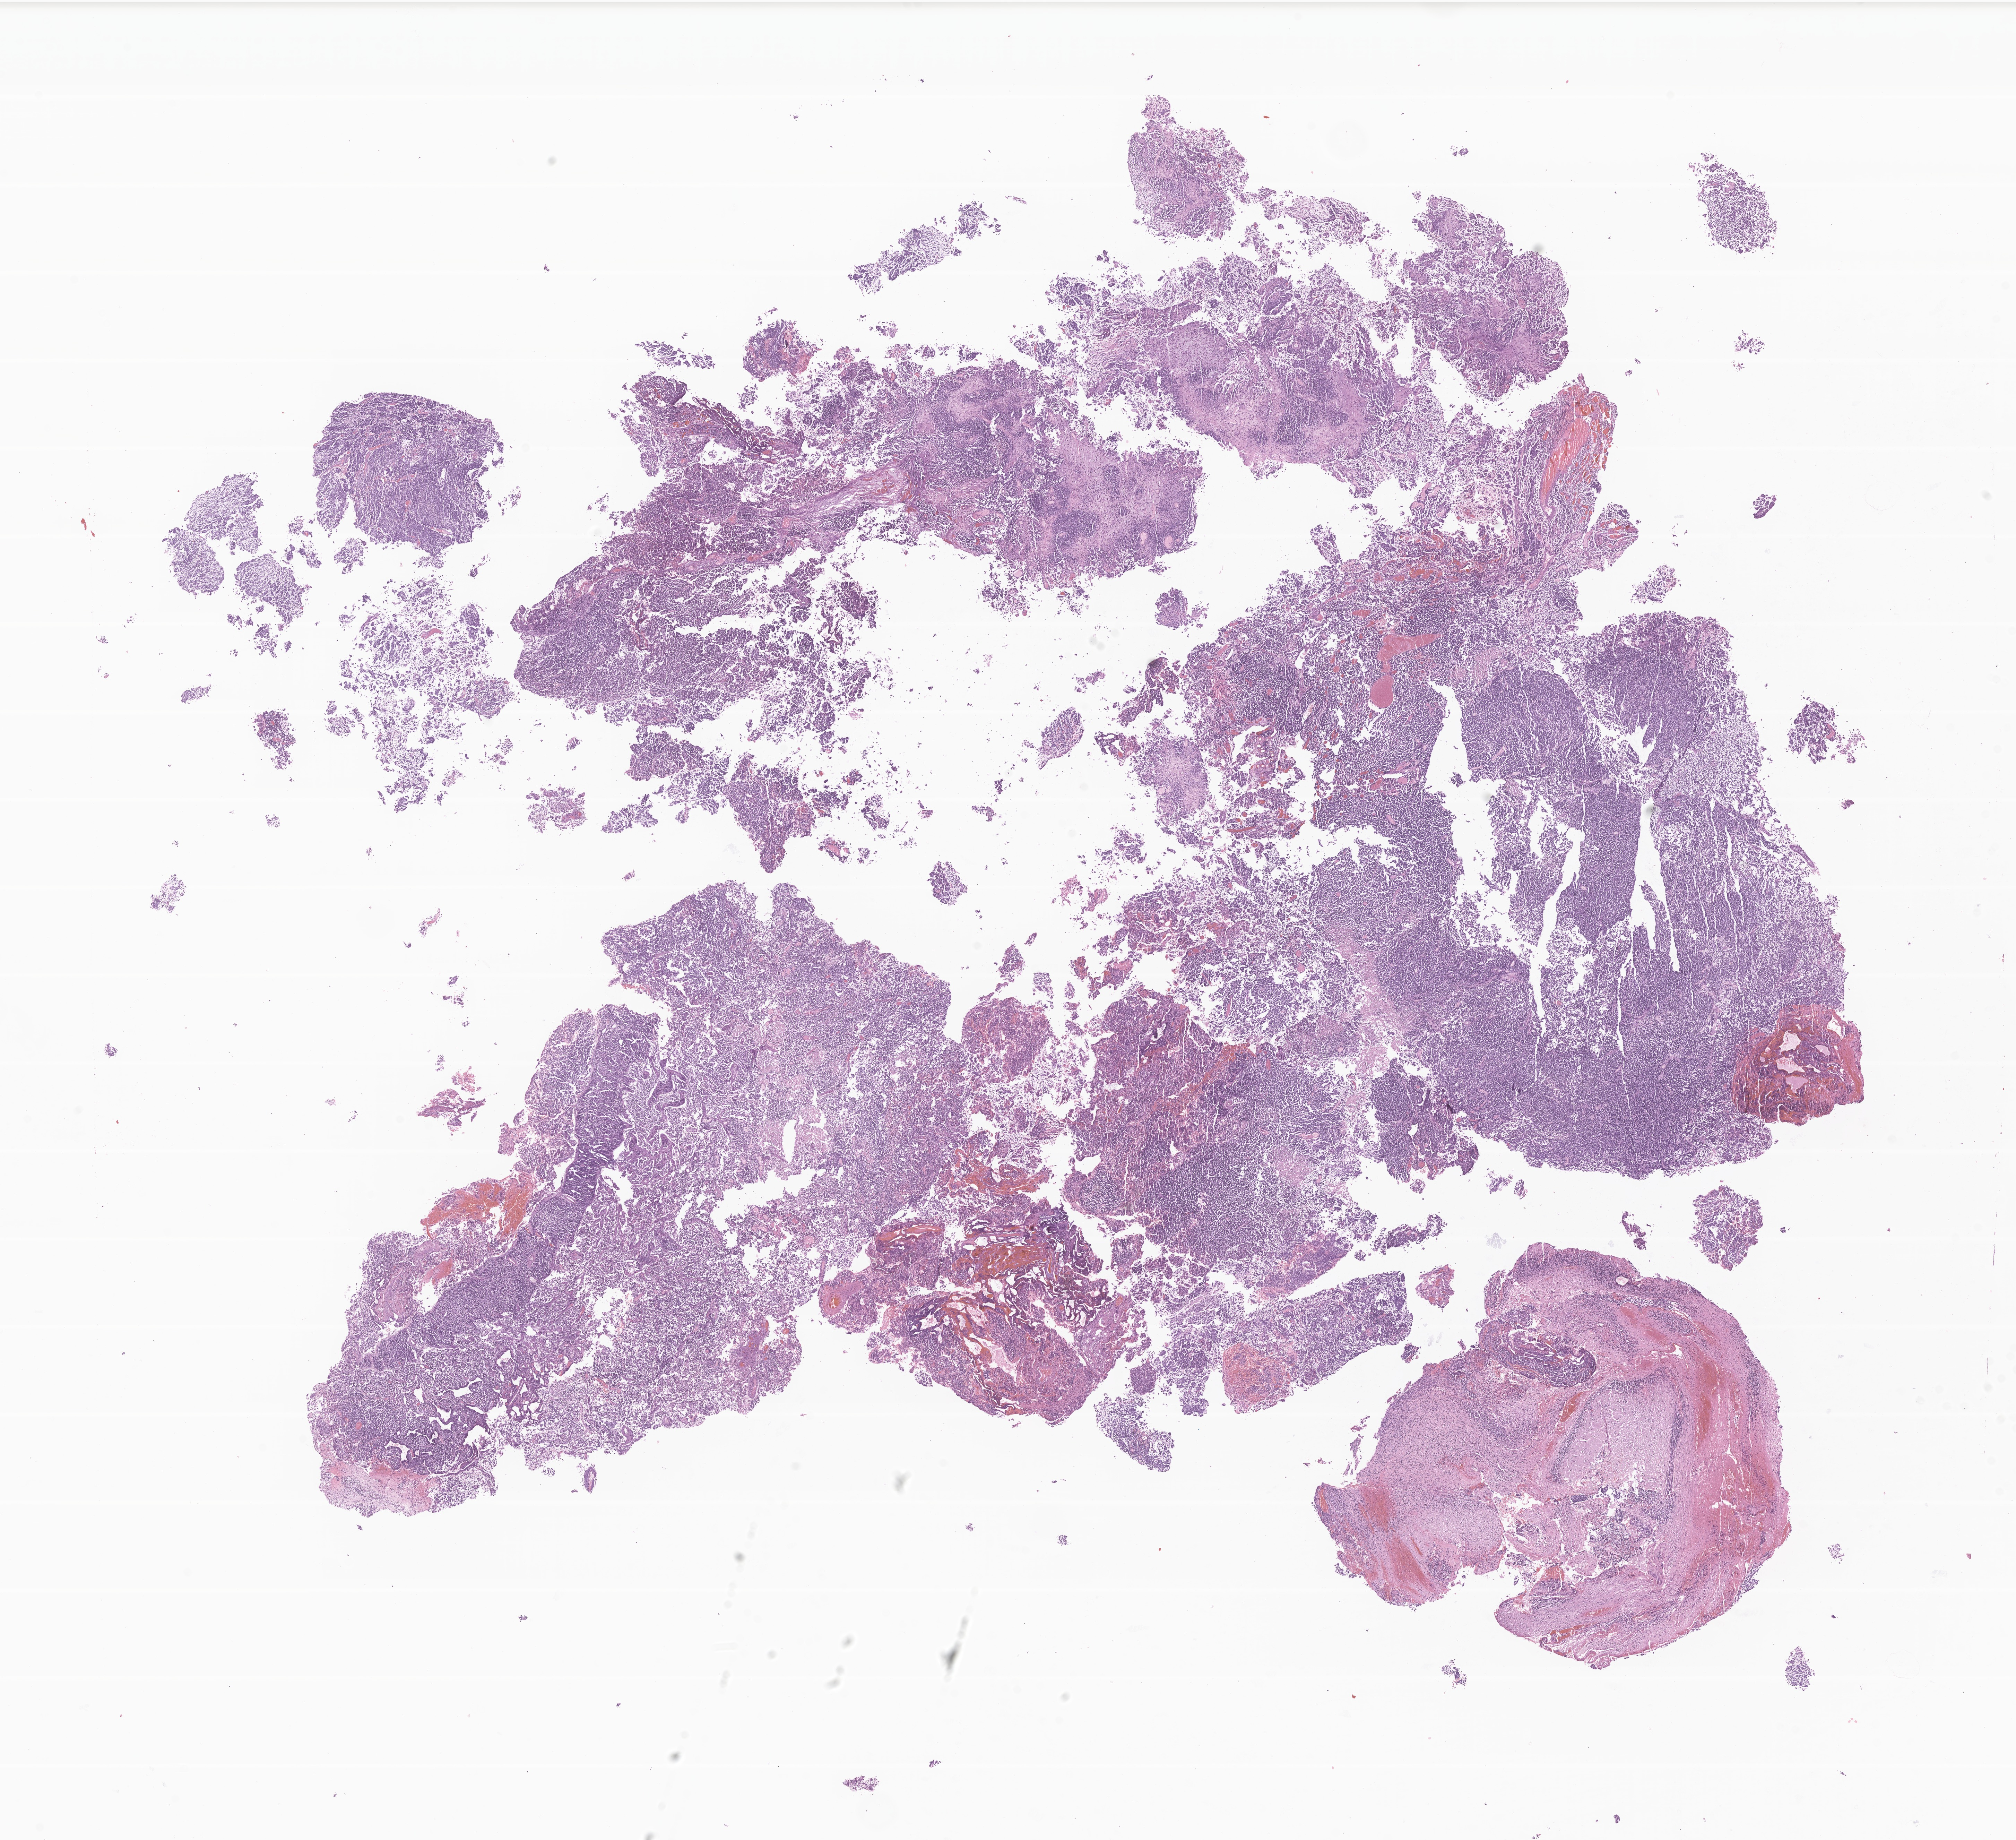
H&E whole-slide image of tumor tissue from the brain, a low-resolution overview of the entire scanned area, about 24.5 x 22.4 mm, FFPE section. Patient male; age 43 months (3 years 7 months).
* diagnosis (ICD-O-3 morphology term): Medulloblastoma, NOS